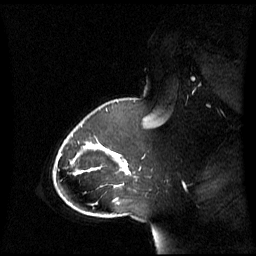
Breast MRI (dynamic contrast-enhanced), one sagittal slice. Slice 46 of 60 in the series (ordered by position). Dynamic contrast-enhanced series, image 2 of 3 at this slice position (ordered by acquisition). 1.5 T. TE 4.2 ms, TR 8.4 ms. 2.8 mm slice thickness. 256 × 256 image matrix. Patient: female, 43 years. From the clinical record (not read from this slice): setting: breast cancer imaged before/during neoadjuvant chemotherapy; receptor status: triple-negative.
Structures marked on this image (semi-automatic segmentation, software-assisted and operator-edited):
- analysis volume of interest (the breast-tissue region the enhancement analysis was run in; not a lesion): box from (x=65, y=118) to (x=143, y=198) px
- tumour enhancement mask (voxels above the 70 % enhancement threshold inside the analysis volume of interest): (x=99, y=145)–(x=128, y=167)